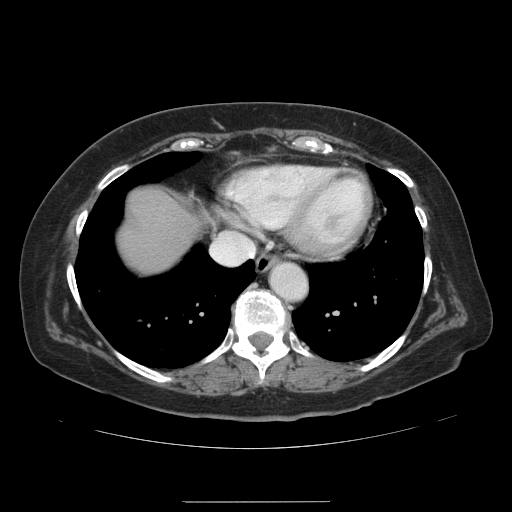
Contrast-enhanced abdominal CT, one axial slice; slice 126 of 141 in the series (ordered by position); 120 kVp; intravenous contrast given; soft-tissue window (W 400 / L 40 HU); 2.5 mm slice thickness; 512 × 512 image matrix, field of view 393 × 393 mm. Female patient, age 74 years. From the clinical record (not read from this slice): diagnosis: colorectal cancer liver metastases, imaged before liver resection; multiple liver metastases: yes; largest metastasis: 7 cm; disease in both lobes: yes.
Outlined on this slice (manually delineated by an expert):
- hepatic veins: bounding box <223,232,232,234> (left, top, right, bottom; pixels)
- liver: <121,191,205,273>
- planned liver remnant (the part of the liver to remain after resection): <122,191,205,273>